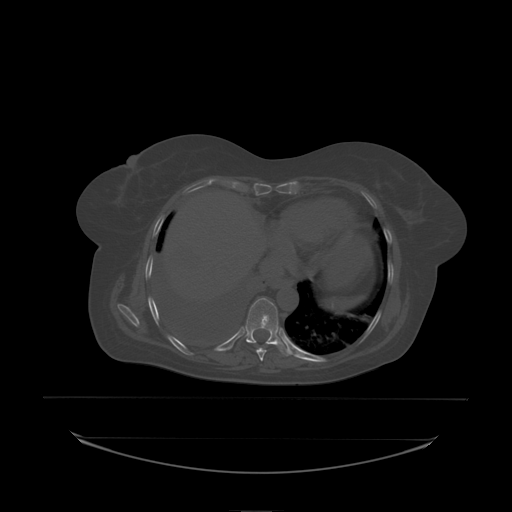
CT including the spine, one axial slice. Position 127 of 242 along the scan axis. Bone window (W 1800 / L 400 HU). 512 × 512 image matrix. Female patient, age 53 years. Case-level facts recorded for this patient, not image findings: primary cancer: lung; vertebrae with lytic lesions (as recorded): T7, L1.
Outlined on this slice (semi-automatically segmented with operator editing):
- T9 vertebra: bounding box [x1, y1, x2, y2] px = [245, 298, 279, 338]